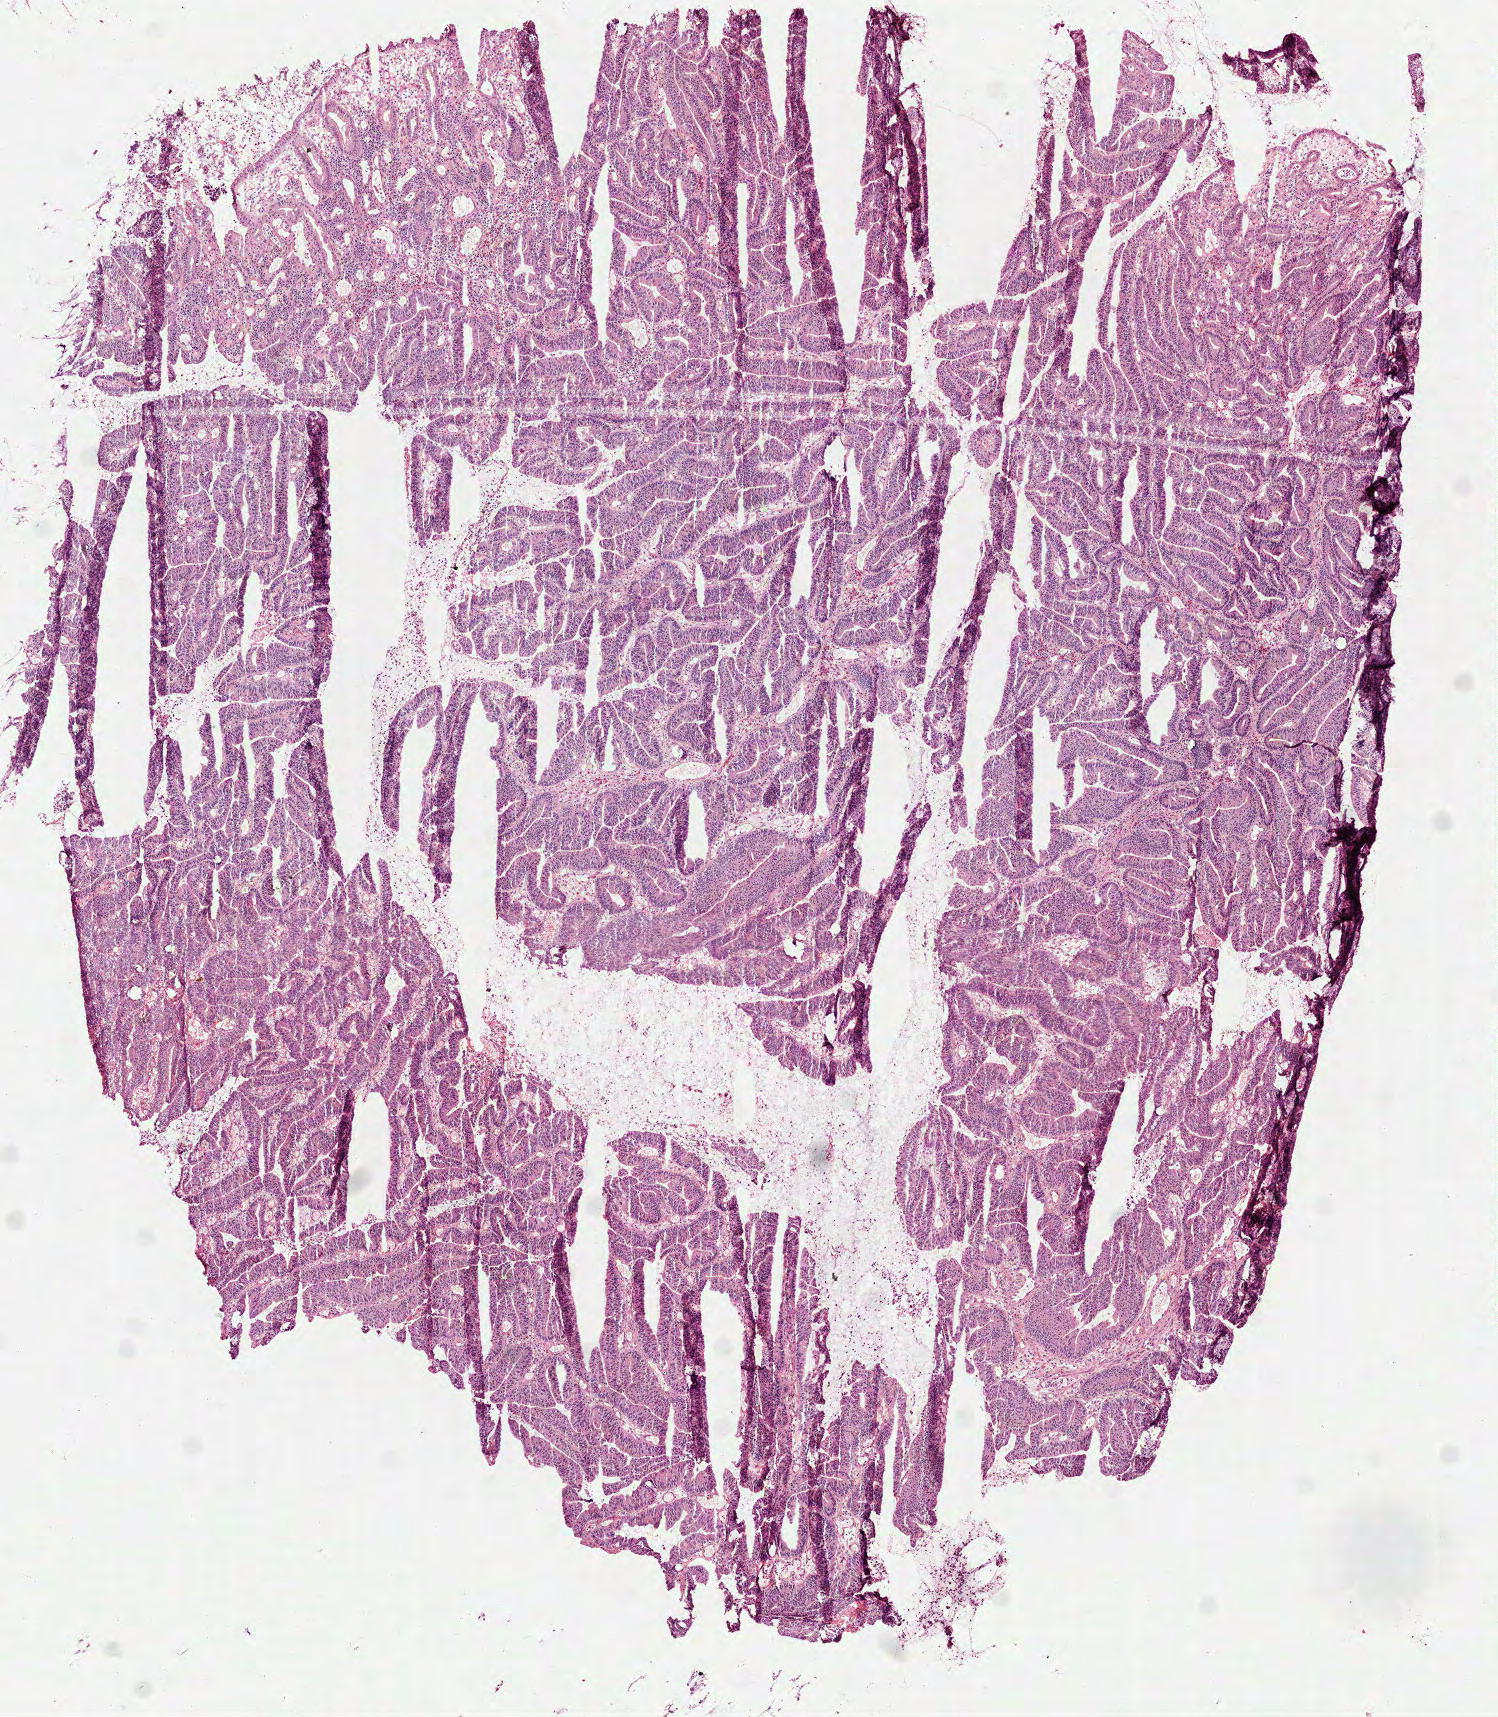
Digitized H&E tissue section (whole slide), a low-resolution overview of the entire scanned area, about 6.0 x 6.9 mm; frozen section from the top of the tissue portion; rectum, primary tumour sample. Patient: male, age at initial diagnosis 59 years. Pathologist review of this section (percent, as recorded): tumour cells 93%, tumour nuclei 85%.
Diagnosis: Adenocarcinoma with mixed subtypes.